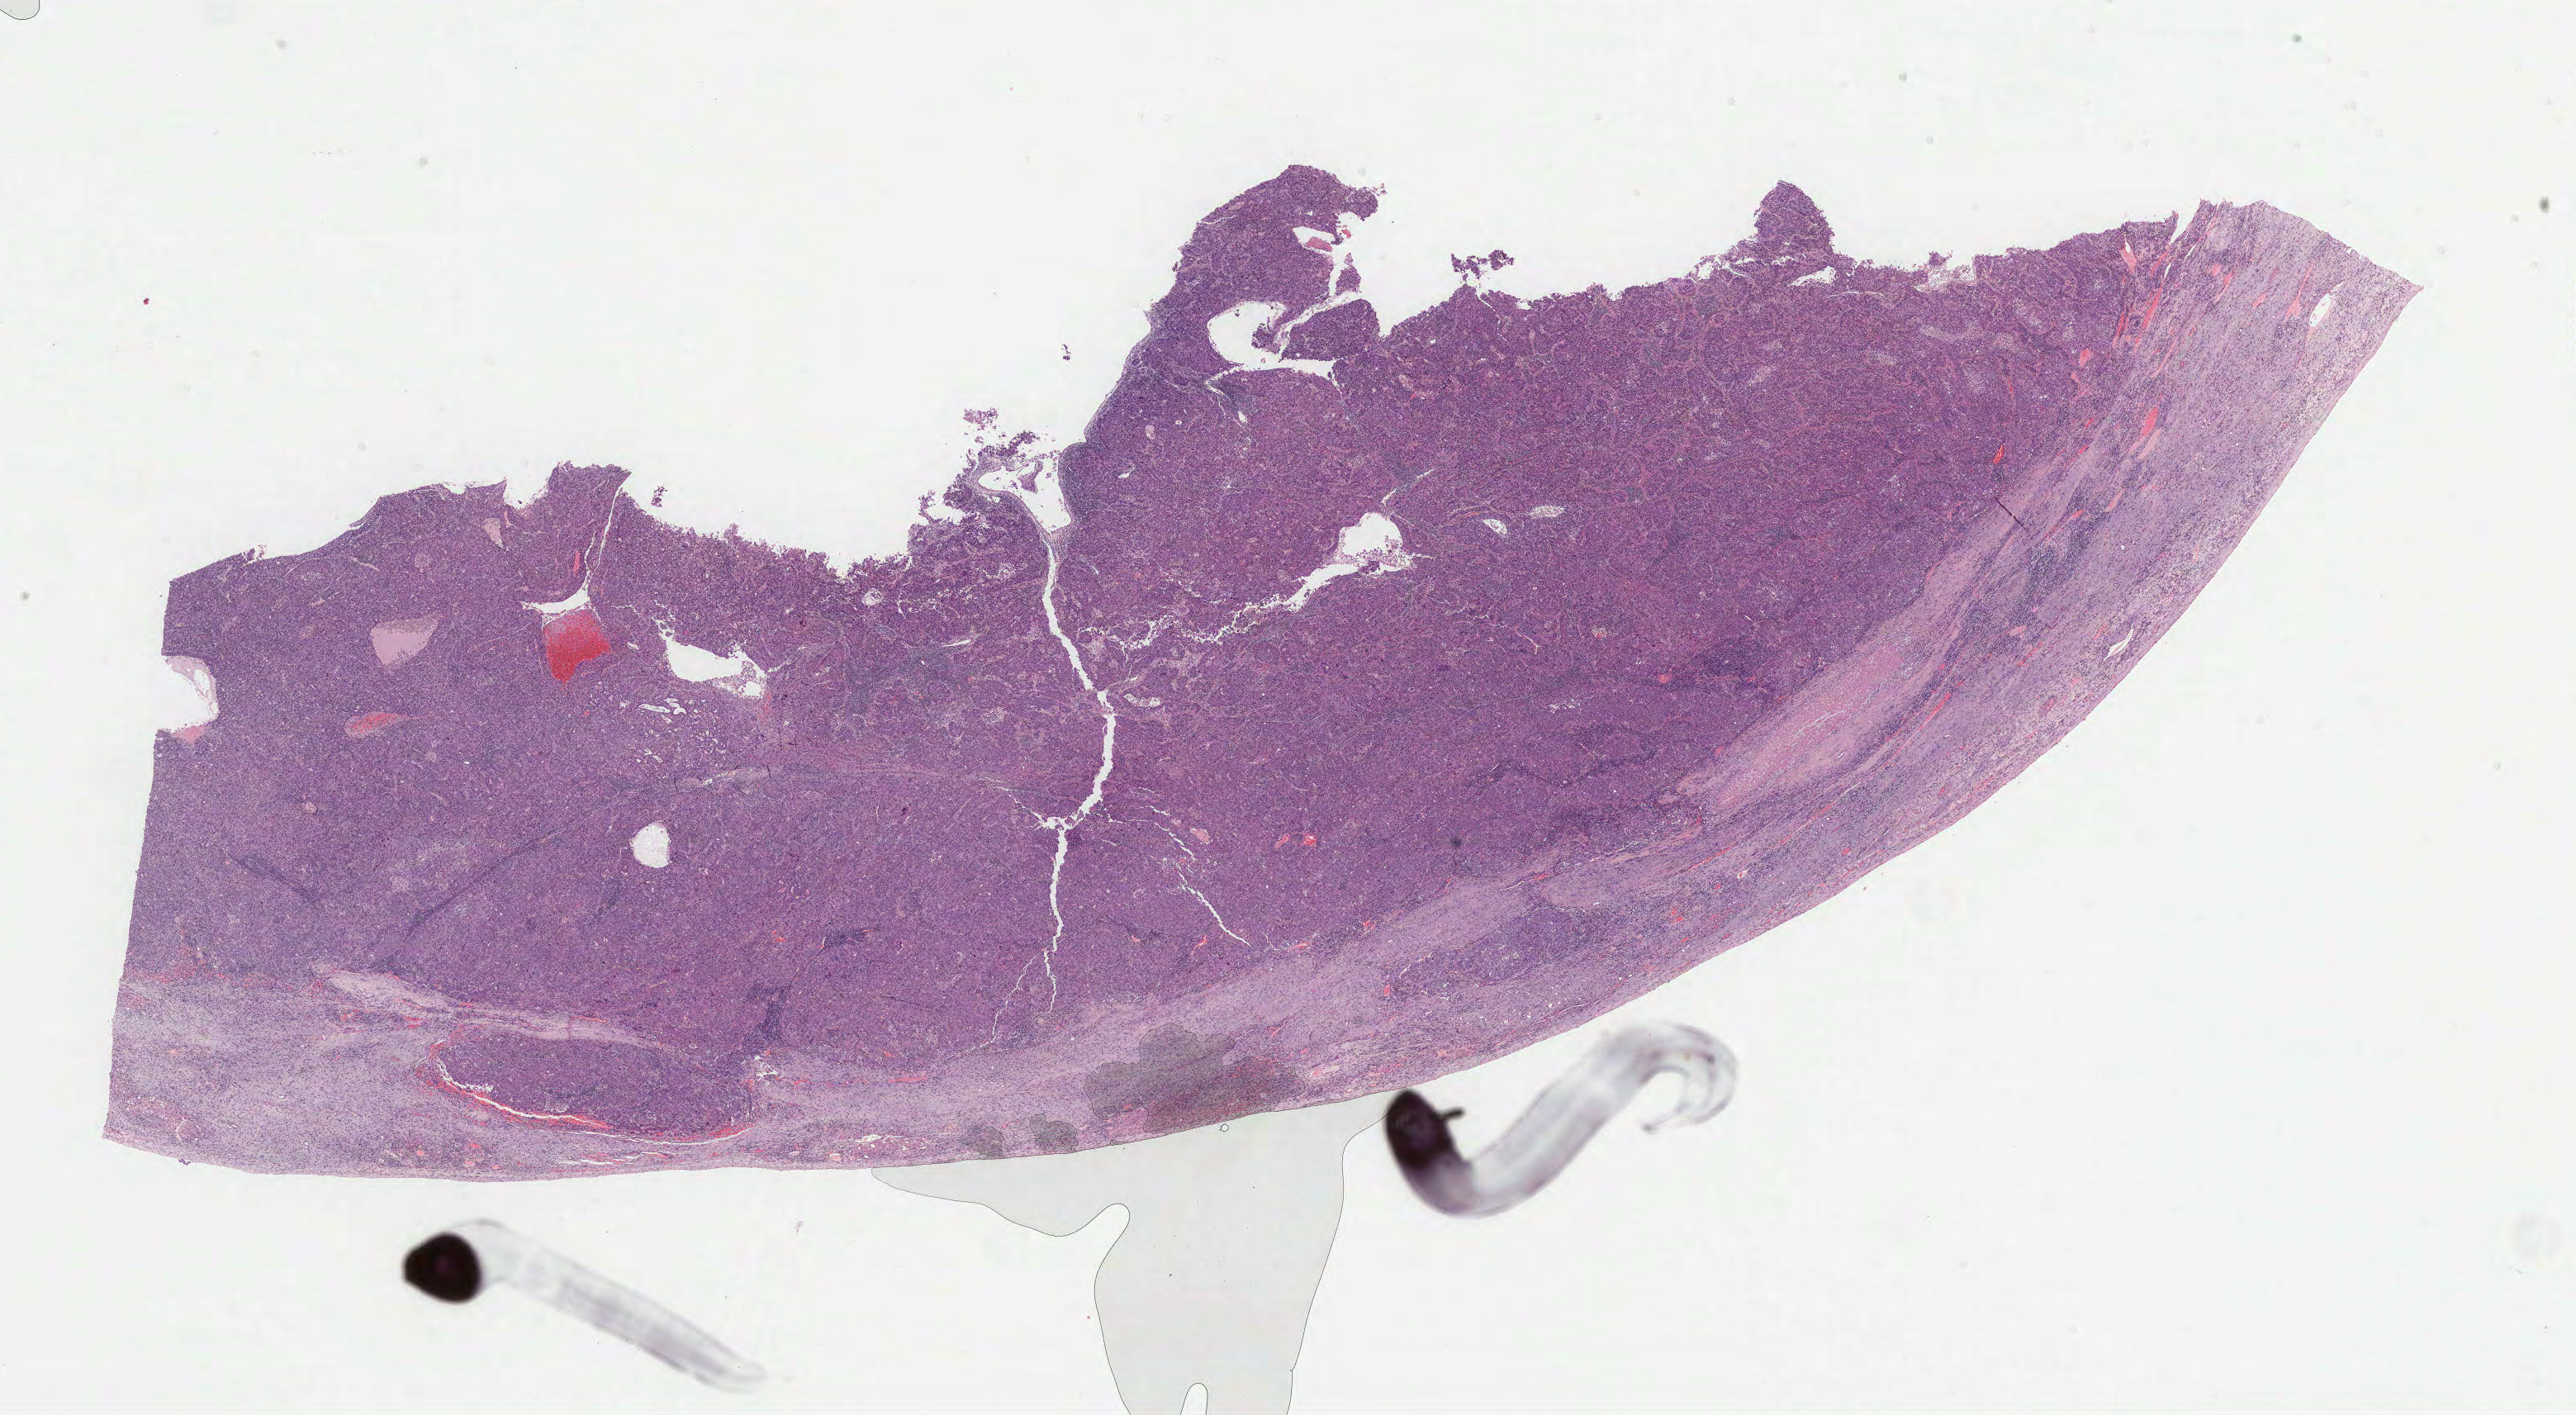
Whole-slide histology image, H&E, shown as a low-resolution overview of the whole scanned area (about 25.2 x 13.8 mm); FFPE section; primary tumour sample from the liver. Female, age 64 years at initial diagnosis.
Histologic diagnosis: Hepatocellular carcinoma, NOS.